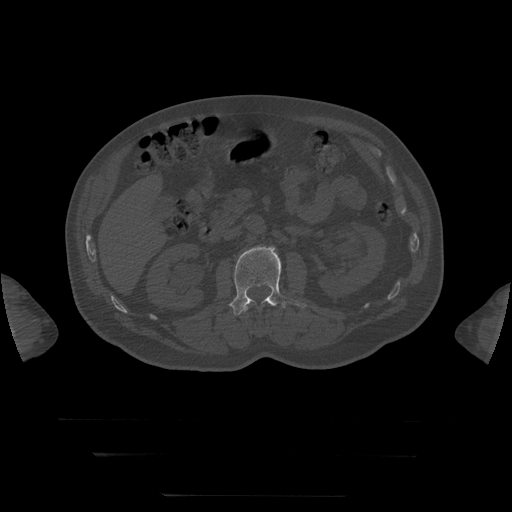
CT including the spine, one axial slice; reconstruction kernel STANDARD; 120 kVp; bone window (W 1800 / L 400 HU); 1.25 mm slice thickness; 512 × 512 image matrix, field of view 510 × 510 mm. Patient age 73 years. Case-level facts recorded for this patient, not image findings: primary cancer: prostate.
Annotated regions visible in this slice (semi-automatically segmented with operator editing):
- L1 vertebra: box from (x=244, y=301) to (x=269, y=313) px